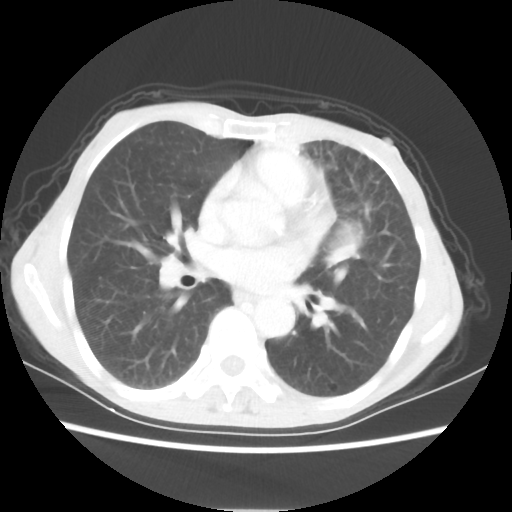
Chest CT, one axial slice. Slice 30 of 56 in the series (ordered by position). Lung window (W 1500 / L -600 HU). 5 mm slice thickness. 512 × 512 image matrix. Patient: female, 60 years. Case-level facts recorded for this patient, not image findings: clinical TNM (as recorded): T4 N1 M0.
Structures marked on this image (bounding box drawn by a radiologist):
- lung tumour (recorded histology: adenocarcinoma): box from (x=326, y=236) to (x=364, y=268) px